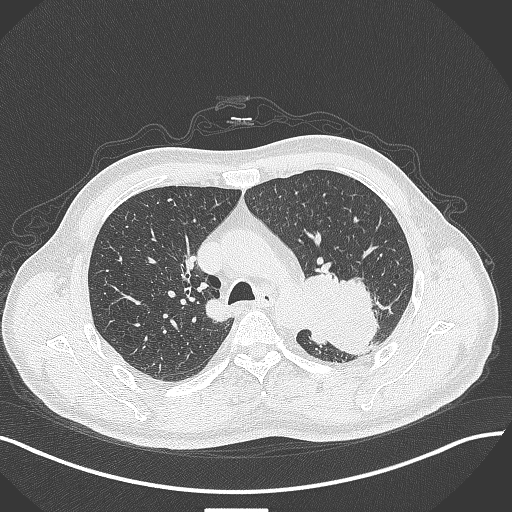
Chest CT, one axial slice. Position 296 of 429 along the scan axis. Reconstruction kernel B70f. 120 kVp. Lung window (W 1500 / L -600 HU). 512 × 512 image matrix, field of view 400 × 400 mm. Male patient, age 55 years. From the clinical record (not read from this slice): clinical TNM (as recorded): T3 N0 M1c.
Structures marked on this image (bounding box drawn by a radiologist):
- lung tumour (recorded histology: adenocarcinoma): bounding box <301,265,380,361> (left, top, right, bottom; pixels)